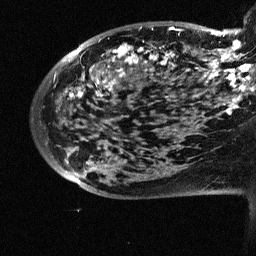
Breast MRI (dynamic contrast-enhanced), one sagittal slice. Position 17 of 64 along the scan axis. Dynamic contrast-enhanced study with each time point stored as its own series, time point 2 of 3 at this slice position (early post-contrast, ordered by acquisition time). 1.5 T. TE 4.5 ms, TR 11 ms. 2.5 mm slice thickness. 256 × 256 image matrix. Patient: female, 38 years. From the clinical record (not read from this slice): setting: breast cancer imaged before/during neoadjuvant chemotherapy; receptor status: HR-positive, HER2-negative.
Structures marked on this image (semi-automatically segmented with operator editing):
- analysis volume of interest (the breast-tissue region the enhancement analysis was run in; not a lesion): bounding box (x1, y1, x2, y2) in pixels: (88, 18, 252, 126)
- tumour enhancement mask (voxels above the 90 % enhancement threshold inside the analysis volume of interest): (106, 26, 252, 114)